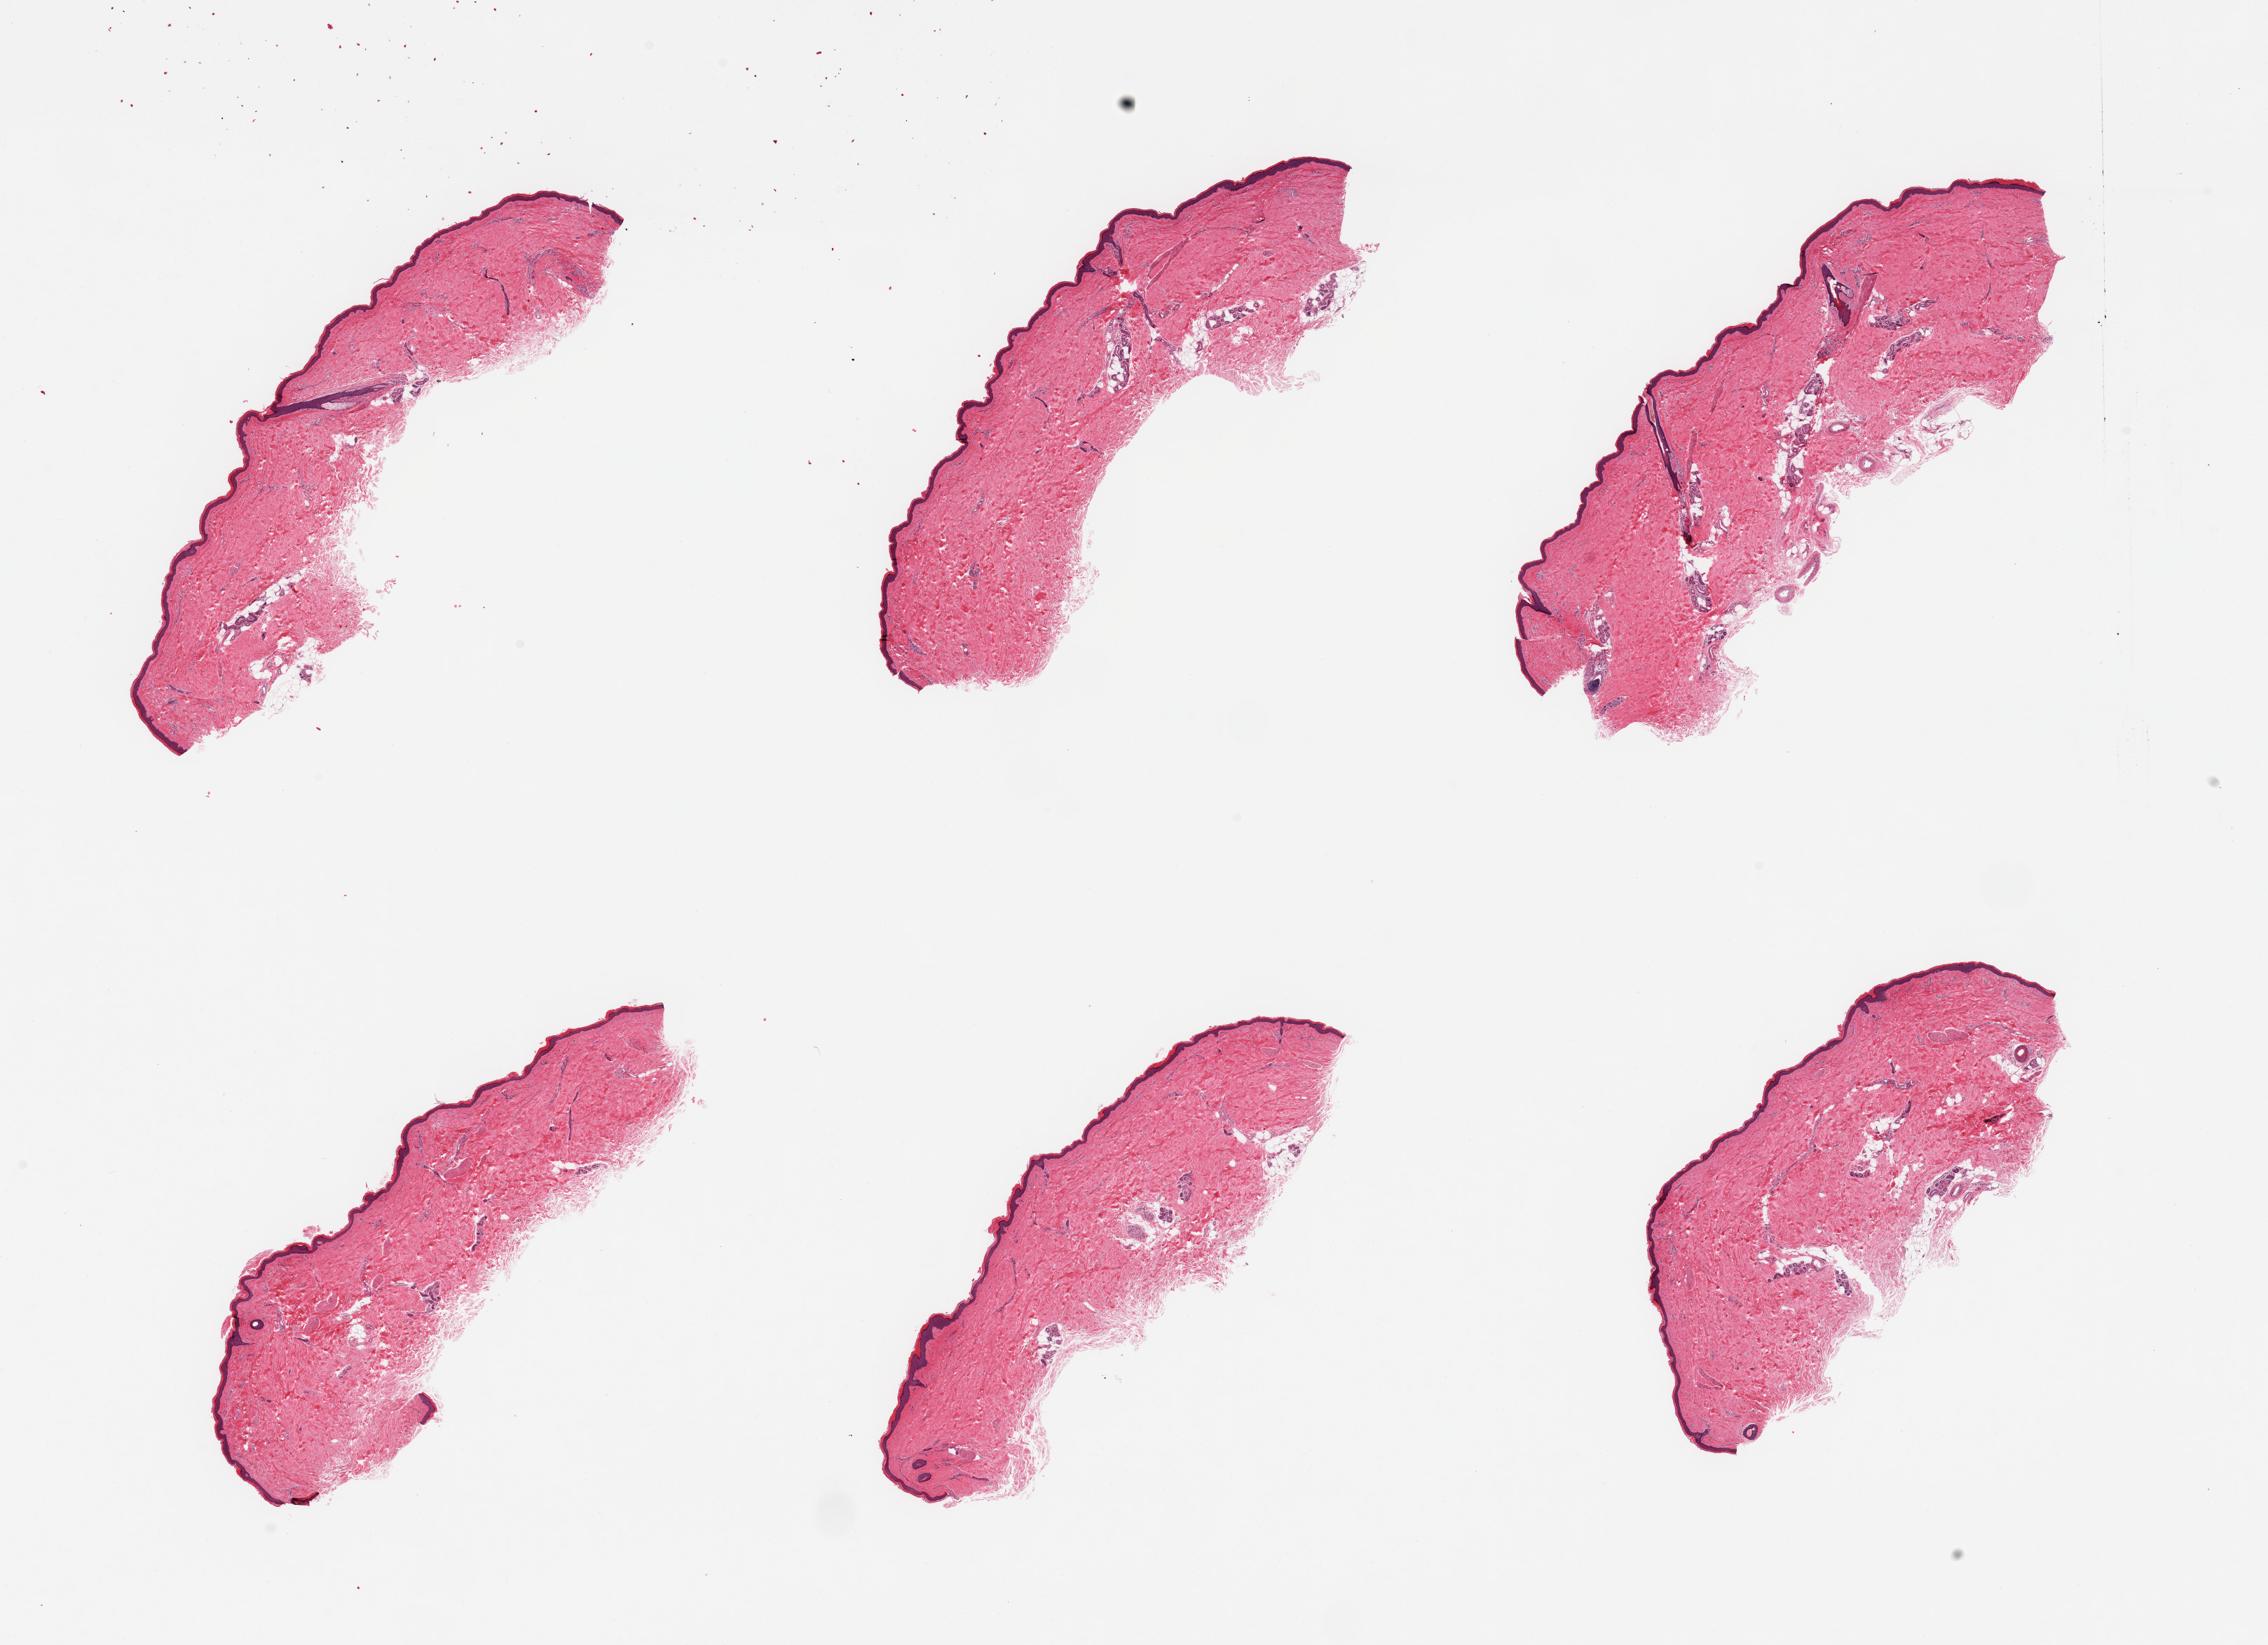
H&E whole-slide image — whole scanned area (about 25.6 x 18.6 mm, acquisition: 20x scan) shown as a low-resolution overview. PAXgene-fixed, paraffin-embedded tissue. Sampled site (target tissue): skin of lower leg. Donor tissue sample.
Pathologist's review note for this sample: 6 pieces; ~47 micron thick epidermis; ~10% periadnexal fat.